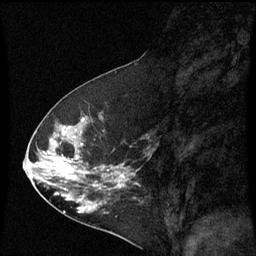
Breast MRI (dynamic contrast-enhanced), one sagittal slice. Position 29 of 60 along the scan axis. Dynamic contrast-enhanced series, image 2 of 3 at this slice position (ordered by acquisition). 1.5 T. TE 4.2 ms, TR 8.9 ms. 2 mm slice thickness. 256 × 256 image matrix, field of view 200 × 200 mm. Patient: female, 53 years. Case-level facts recorded for this patient, not image findings: setting: breast cancer imaged before/during neoadjuvant chemotherapy; receptor status: HR-positive, HER2-negative.
Structures marked on this image (semi-automatic segmentation, software-assisted and operator-edited):
- analysis volume of interest (the breast-tissue region the enhancement analysis was run in; not a lesion): bounding box [x1, y1, x2, y2] px = [32, 100, 145, 221]
- tumour enhancement mask (voxels above the 70 % enhancement threshold inside the analysis volume of interest): [50, 132, 129, 213]